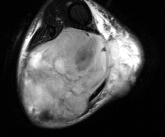
MRI of an extremity soft-tissue mass, one axial slice. Position 36 of 81 along the scan axis. T2-weighted fat-saturated. MR volume resampled by the dataset authors to the PET/CT grid (not the native acquisition matrix). 165 × 137 image matrix. Male patient. Case-level facts recorded for this patient, not image findings: histological type: liposarcoma - round cell; grade: high; site of the primary tumour: right calf.
Outlined on this slice (expert contour drawn on MRI and transferred to this co-registered scan by the dataset authors):
- gross tumour volume (mass): bounding box <21,27,140,120> (left, top, right, bottom; pixels)